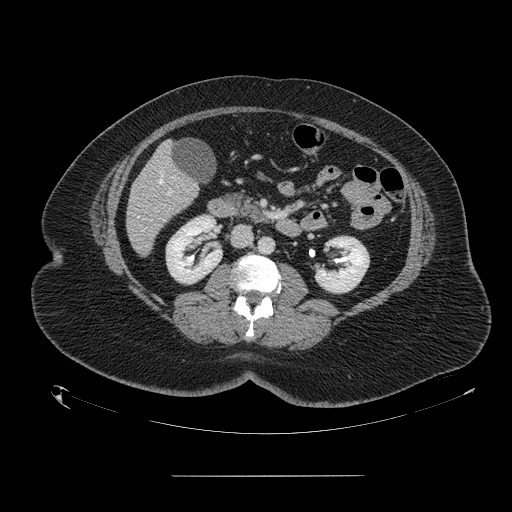
Contrast-enhanced abdominal CT, one axial slice. Slice 53 of 164 in the series (ordered by position). Intravenous contrast given. Soft-tissue window (W 400 / L 40 HU). 2.5 mm slice thickness. 512 × 512 image matrix. Female patient, age 52 years. Case-level facts recorded for this patient, not image findings: diagnosis: colorectal cancer liver metastases, imaged before liver resection; multiple liver metastases: yes; largest metastasis: 3.5 cm.
Outlined on this slice (expert manual segmentation):
- hepatic veins: bounding box <138,174,174,217> (left, top, right, bottom; pixels)
- liver: <127,144,199,254>
- portal vein (with intrahepatic branches): <167,193,170,195>